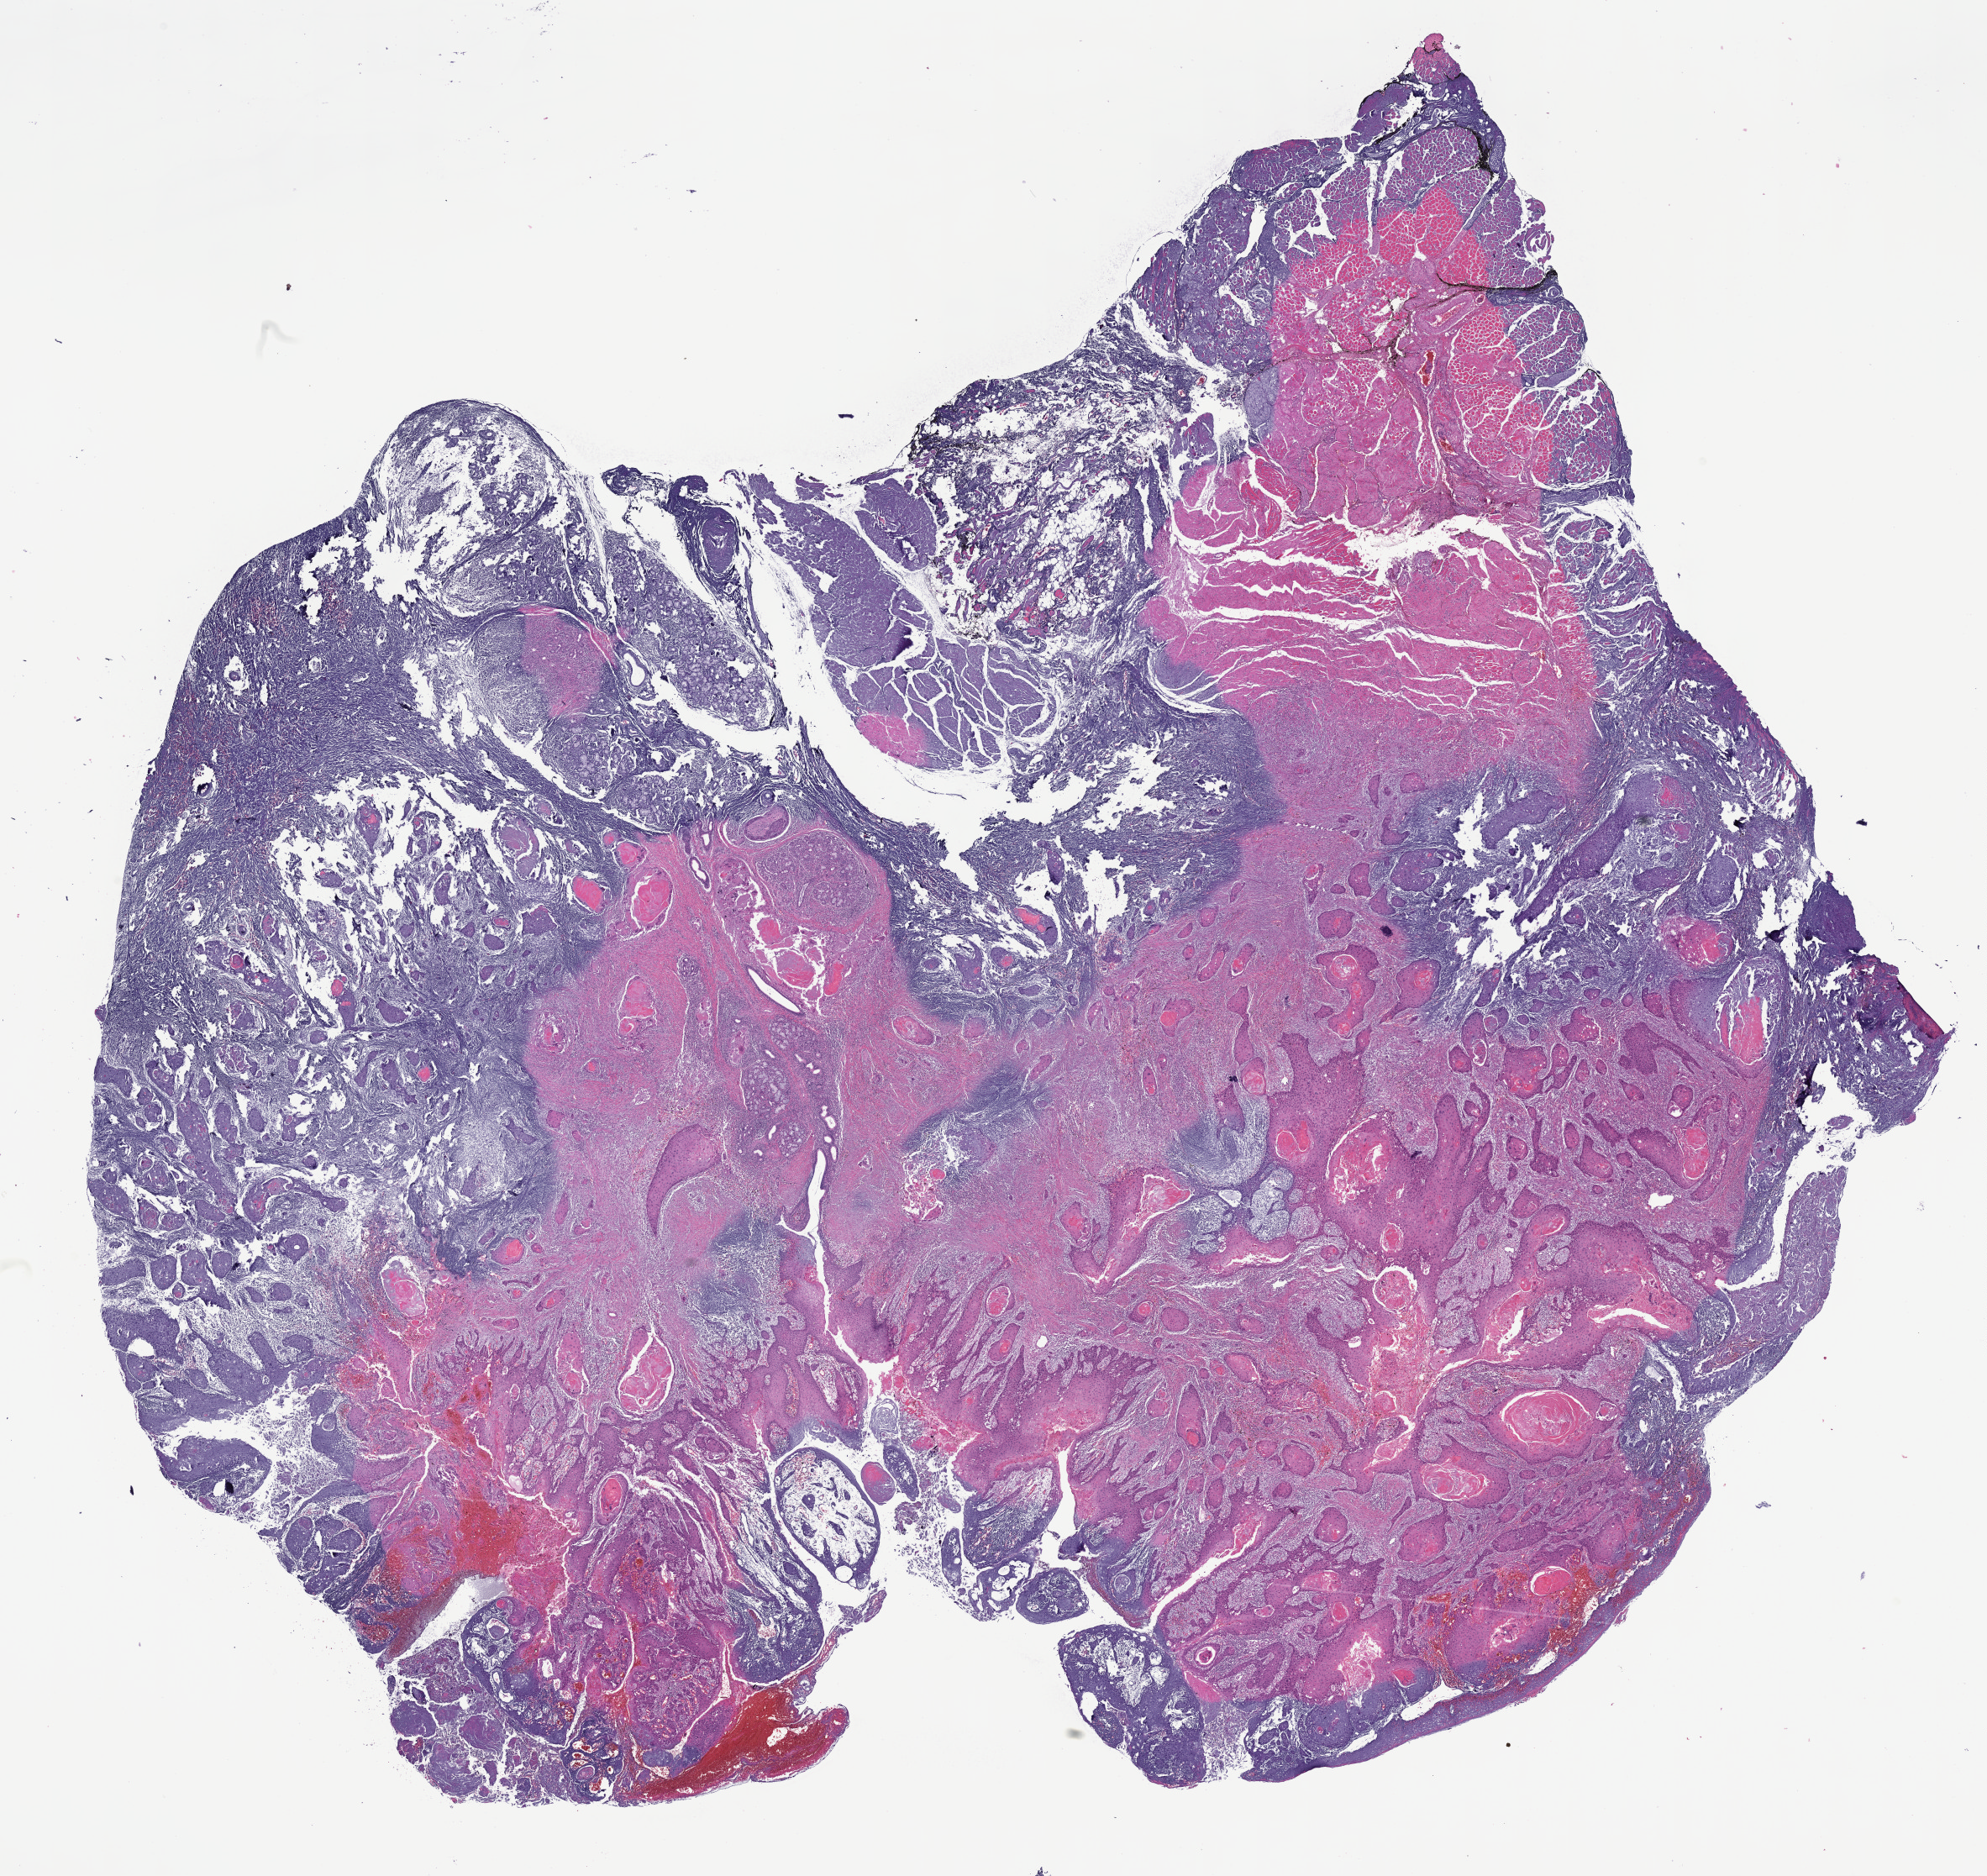
Whole-slide histology image, Hematoxylin and eosin (H&E) stained, shown as a low-resolution overview of the whole scanned area (about 19.1 x 18.1 mm, from a 40x scan); FFPE section; primary tumour sample from the head and neck. Male patient; age at initial diagnosis 57 years. Histologic grade: G2 (moderately differentiated).
• histologic diagnosis: Squamous cell carcinoma, NOS (gum, NOS)